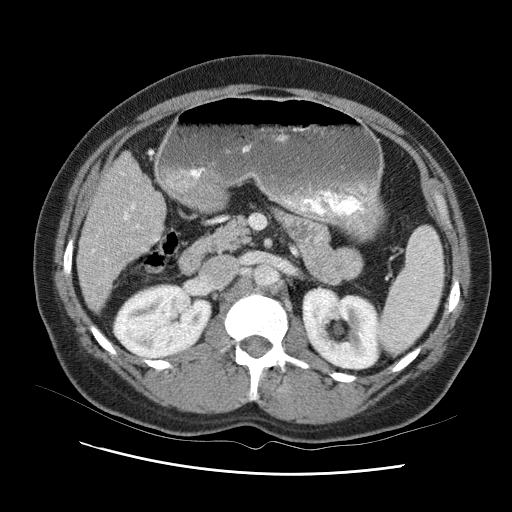
Contrast-enhanced abdominal CT (liver protocol), one axial slice; slice 38 of 95 in the series (ordered by position); reconstruction kernel STANDARD; one of 2 acquisitions stored at this slice position; soft-tissue window (W 400 / L 40 HU); 2.5 mm slice thickness; 512 × 512 image matrix, field of view 360 × 360 mm. From the clinical record (not read from this slice): diagnosis: hepatocellular carcinoma (patient treated with transarterial chemoembolisation; whether this scan precedes or follows treatment is not stated here); TNM stage (as recorded): Stage-I; Child-Pugh class: B; tumour differentiation: moderately differentiated.
Structures marked on this image (semi-automatic segmentation, software-assisted and operator-edited):
- liver parenchyma outside the tumour (the mass and vessels are separate outlines, so this box may not span the whole liver): bounding box (x1, y1, x2, y2) in pixels: (76, 140, 168, 323)
- mass: (122, 264, 169, 300)
- liver vessels: (92, 211, 140, 285)